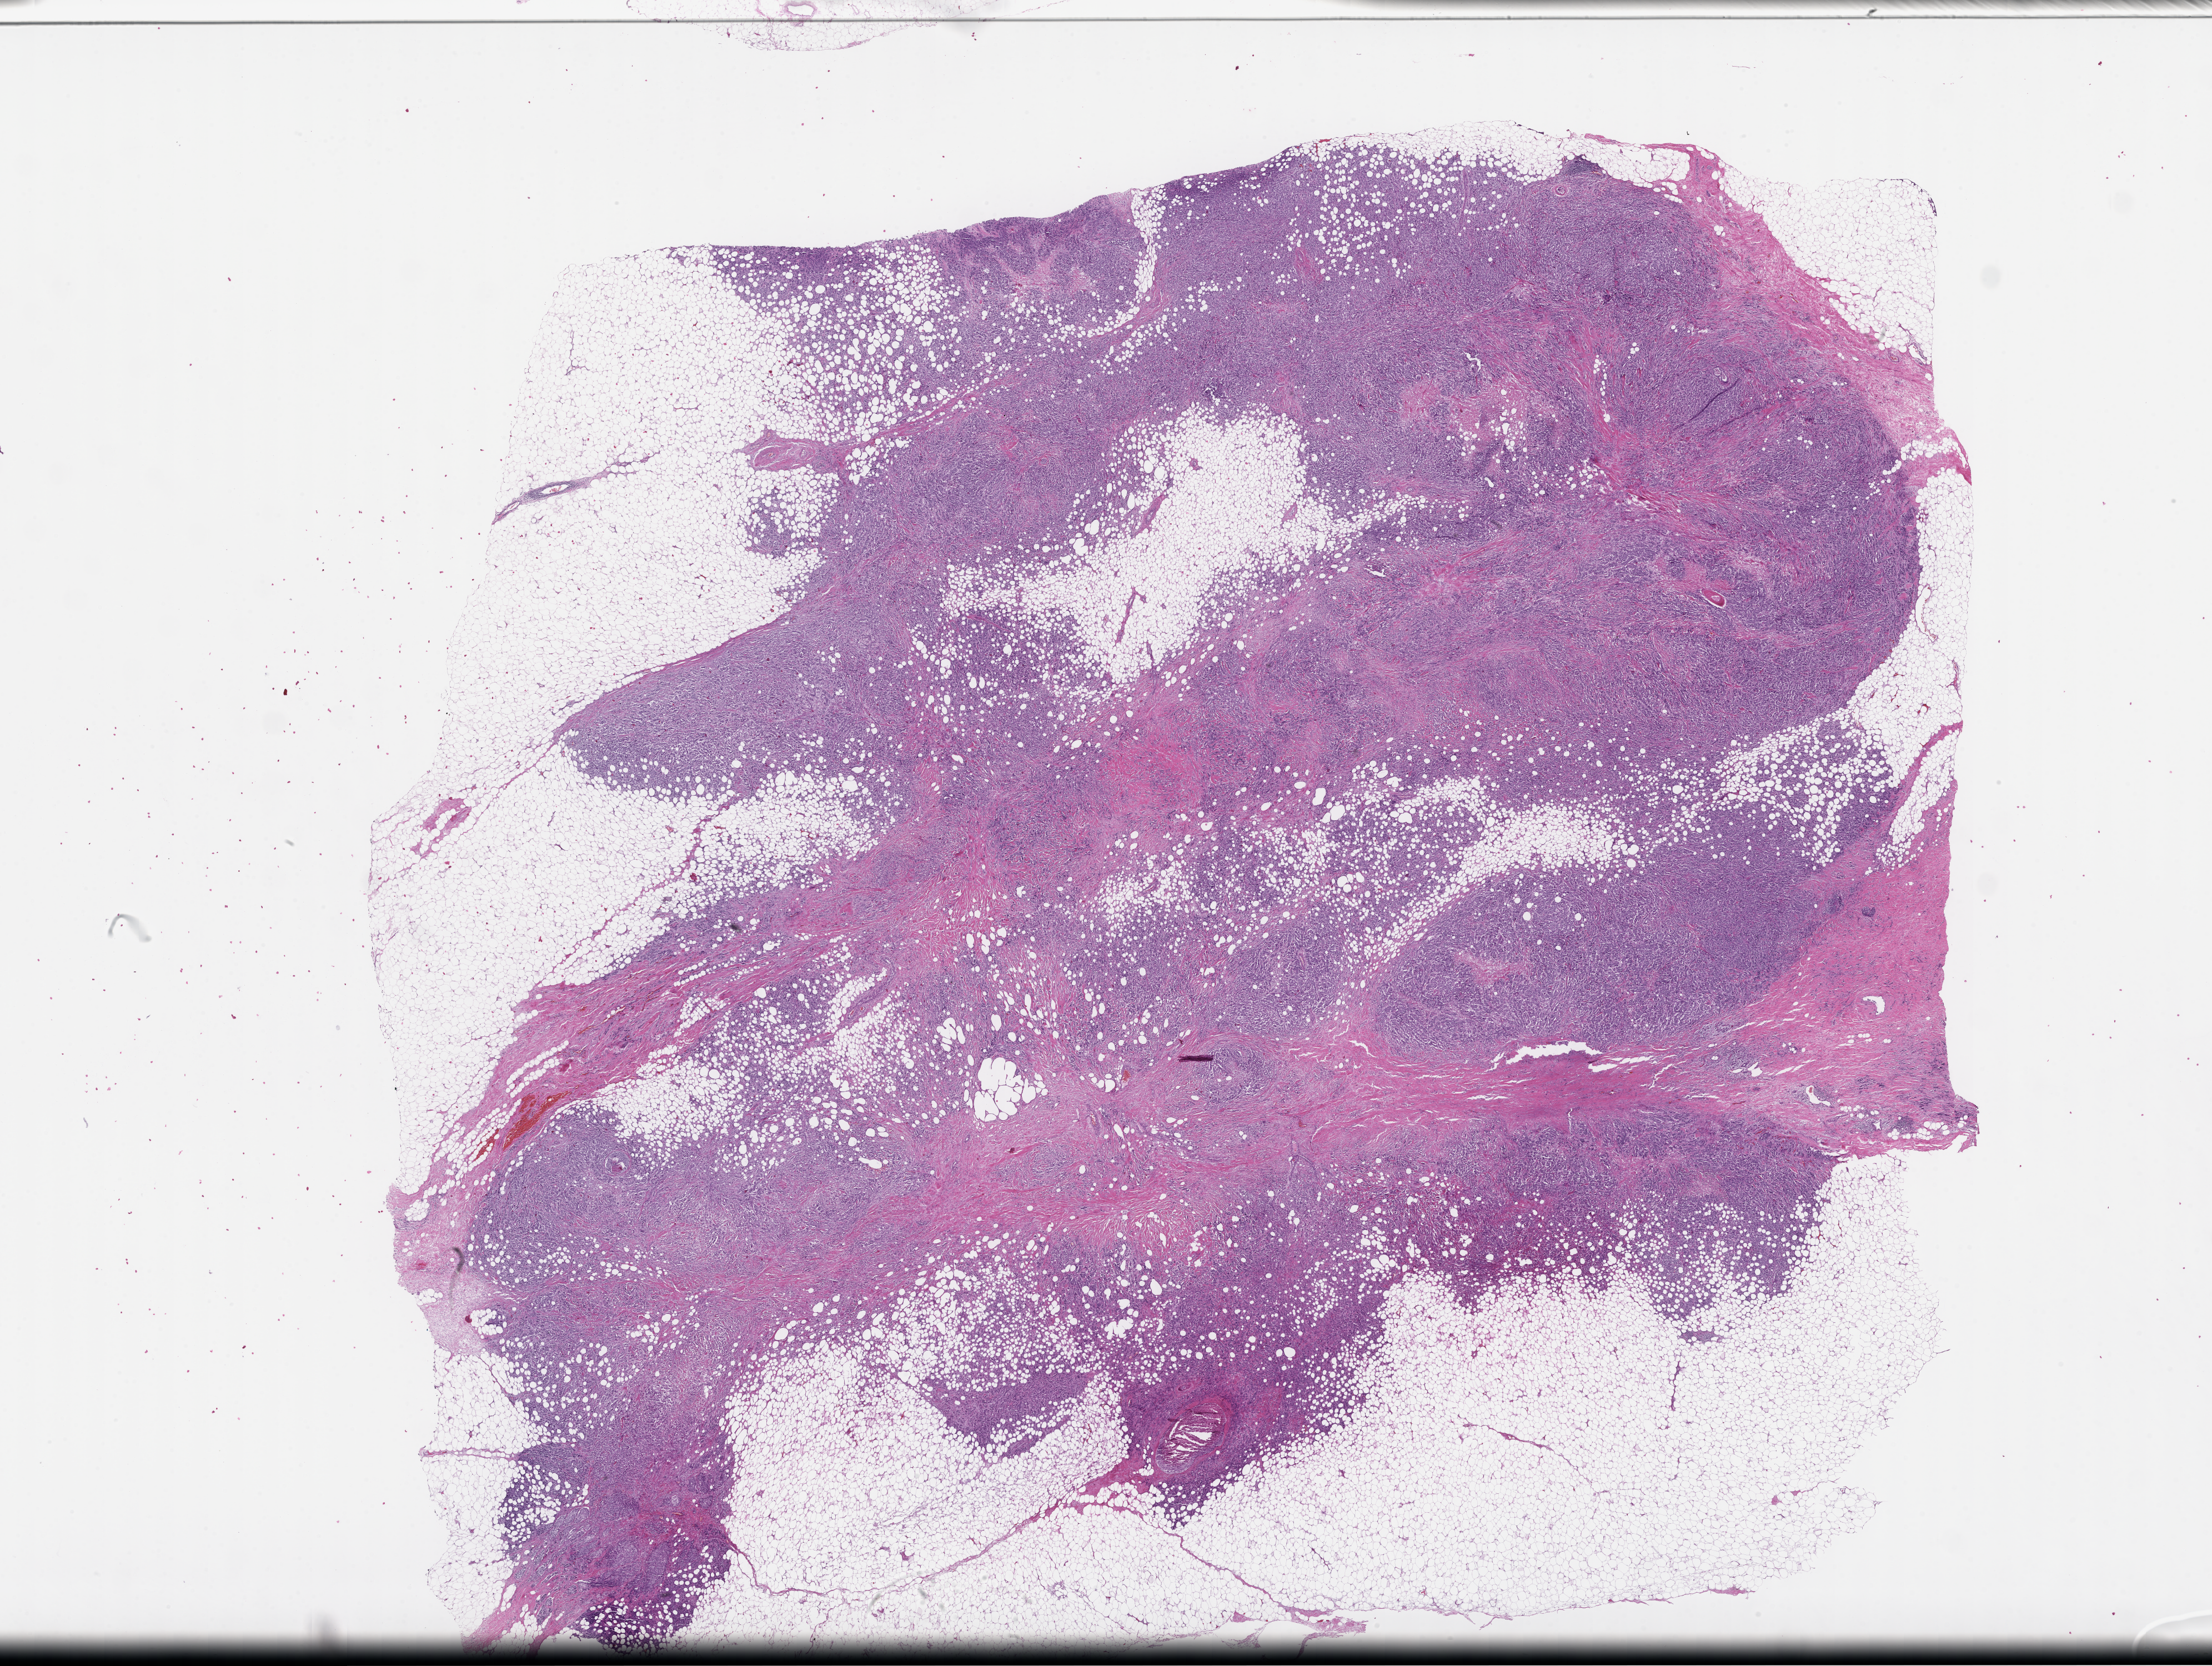
Digitized H&E-stained section — a low-resolution overview of the entire scanned area, about 32.2 x 24.2 mm, FFPE section, tissue site: breast, specimen time point: archival tissue. Female patient.
This section: primary tumour tissue. Diagnosis: Invasive Breast Carcinoma.